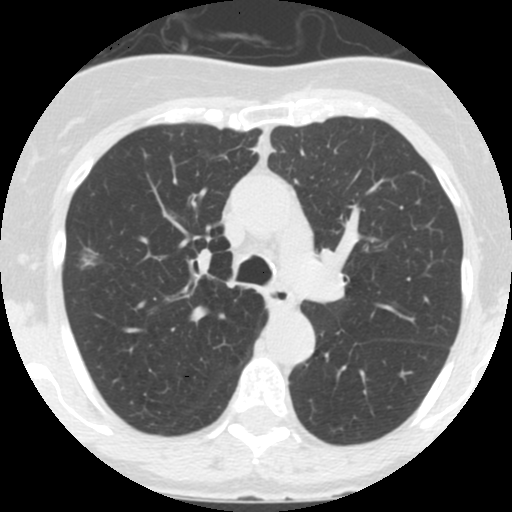
Chest CT (low-dose screening protocol), one axial image. Third annual screen. Lung window (W 1500 / L -600 HU). 2.5 mm slice thickness. 120 kVp. Slice 50 of 146 in the series. Female participant, aged 60 years at enrolment.
Lesion marked by an expert reader, bounding box <59,231,109,283> (left, top, right, bottom; pixels). Reader record for this screening exam (exam-level; its link to the box is not recorded): non-calcified nodule or mass ≥4 mm, right upper lobe, 12 × 12 mm, smooth margins, ground glass attenuation, pre-existing on the prior screen: yes; interval growth: yes. Official screen result: positive, other. Later outcome: lung cancer diagnosed 56 days after this screen — bronchiolo-alveolar adenocarcinoma, NOS, right upper lobe, well differentiated (G1), stage IA (AJCC 6th edition), 11 mm at pathology.